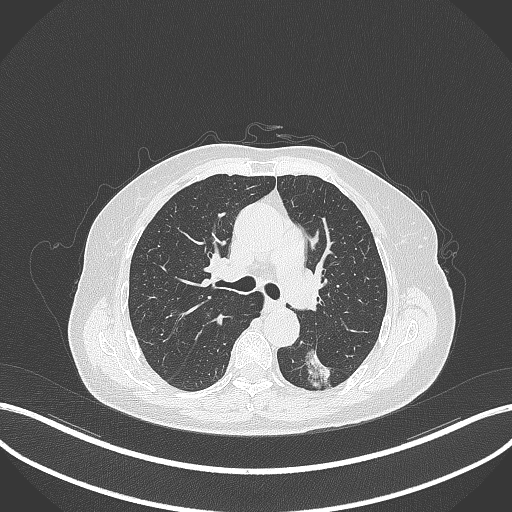
Chest CT, one axial slice; slice 191 of 352 in the series (ordered by position); 120 kVp; lung window (W 1500 / L -600 HU); 1 mm slice thickness; 512 × 512 image matrix, field of view 400 × 400 mm. Female patient, age 70 years. From the clinical record (not read from this slice): clinical TNM (as recorded): T1c N0 M0.
Annotated regions visible in this slice (bounding box drawn by a radiologist):
- lung tumour (recorded histology: adenocarcinoma): bounding box [x1, y1, x2, y2] px = [299, 346, 337, 391]